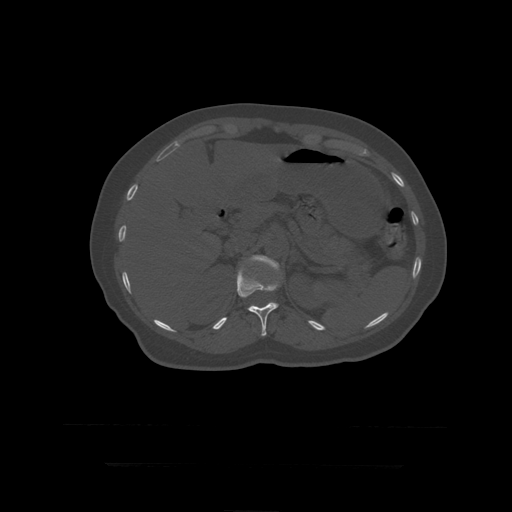
CT including the spine, one axial slice. Position 192 of 399 along the scan axis. Bone window (W 1800 / L 400 HU). 512 × 512 image matrix, field of view 450 × 450 mm. Patient age 41 years. Case-level facts recorded for this patient, not image findings: primary cancer: breast.
Outlined on this slice (semi-automatically segmented with operator editing):
- L1 vertebra: bounding box (x1, y1, x2, y2) in pixels: (250, 255, 280, 271)
- T12 vertebra: (237, 263, 280, 336)